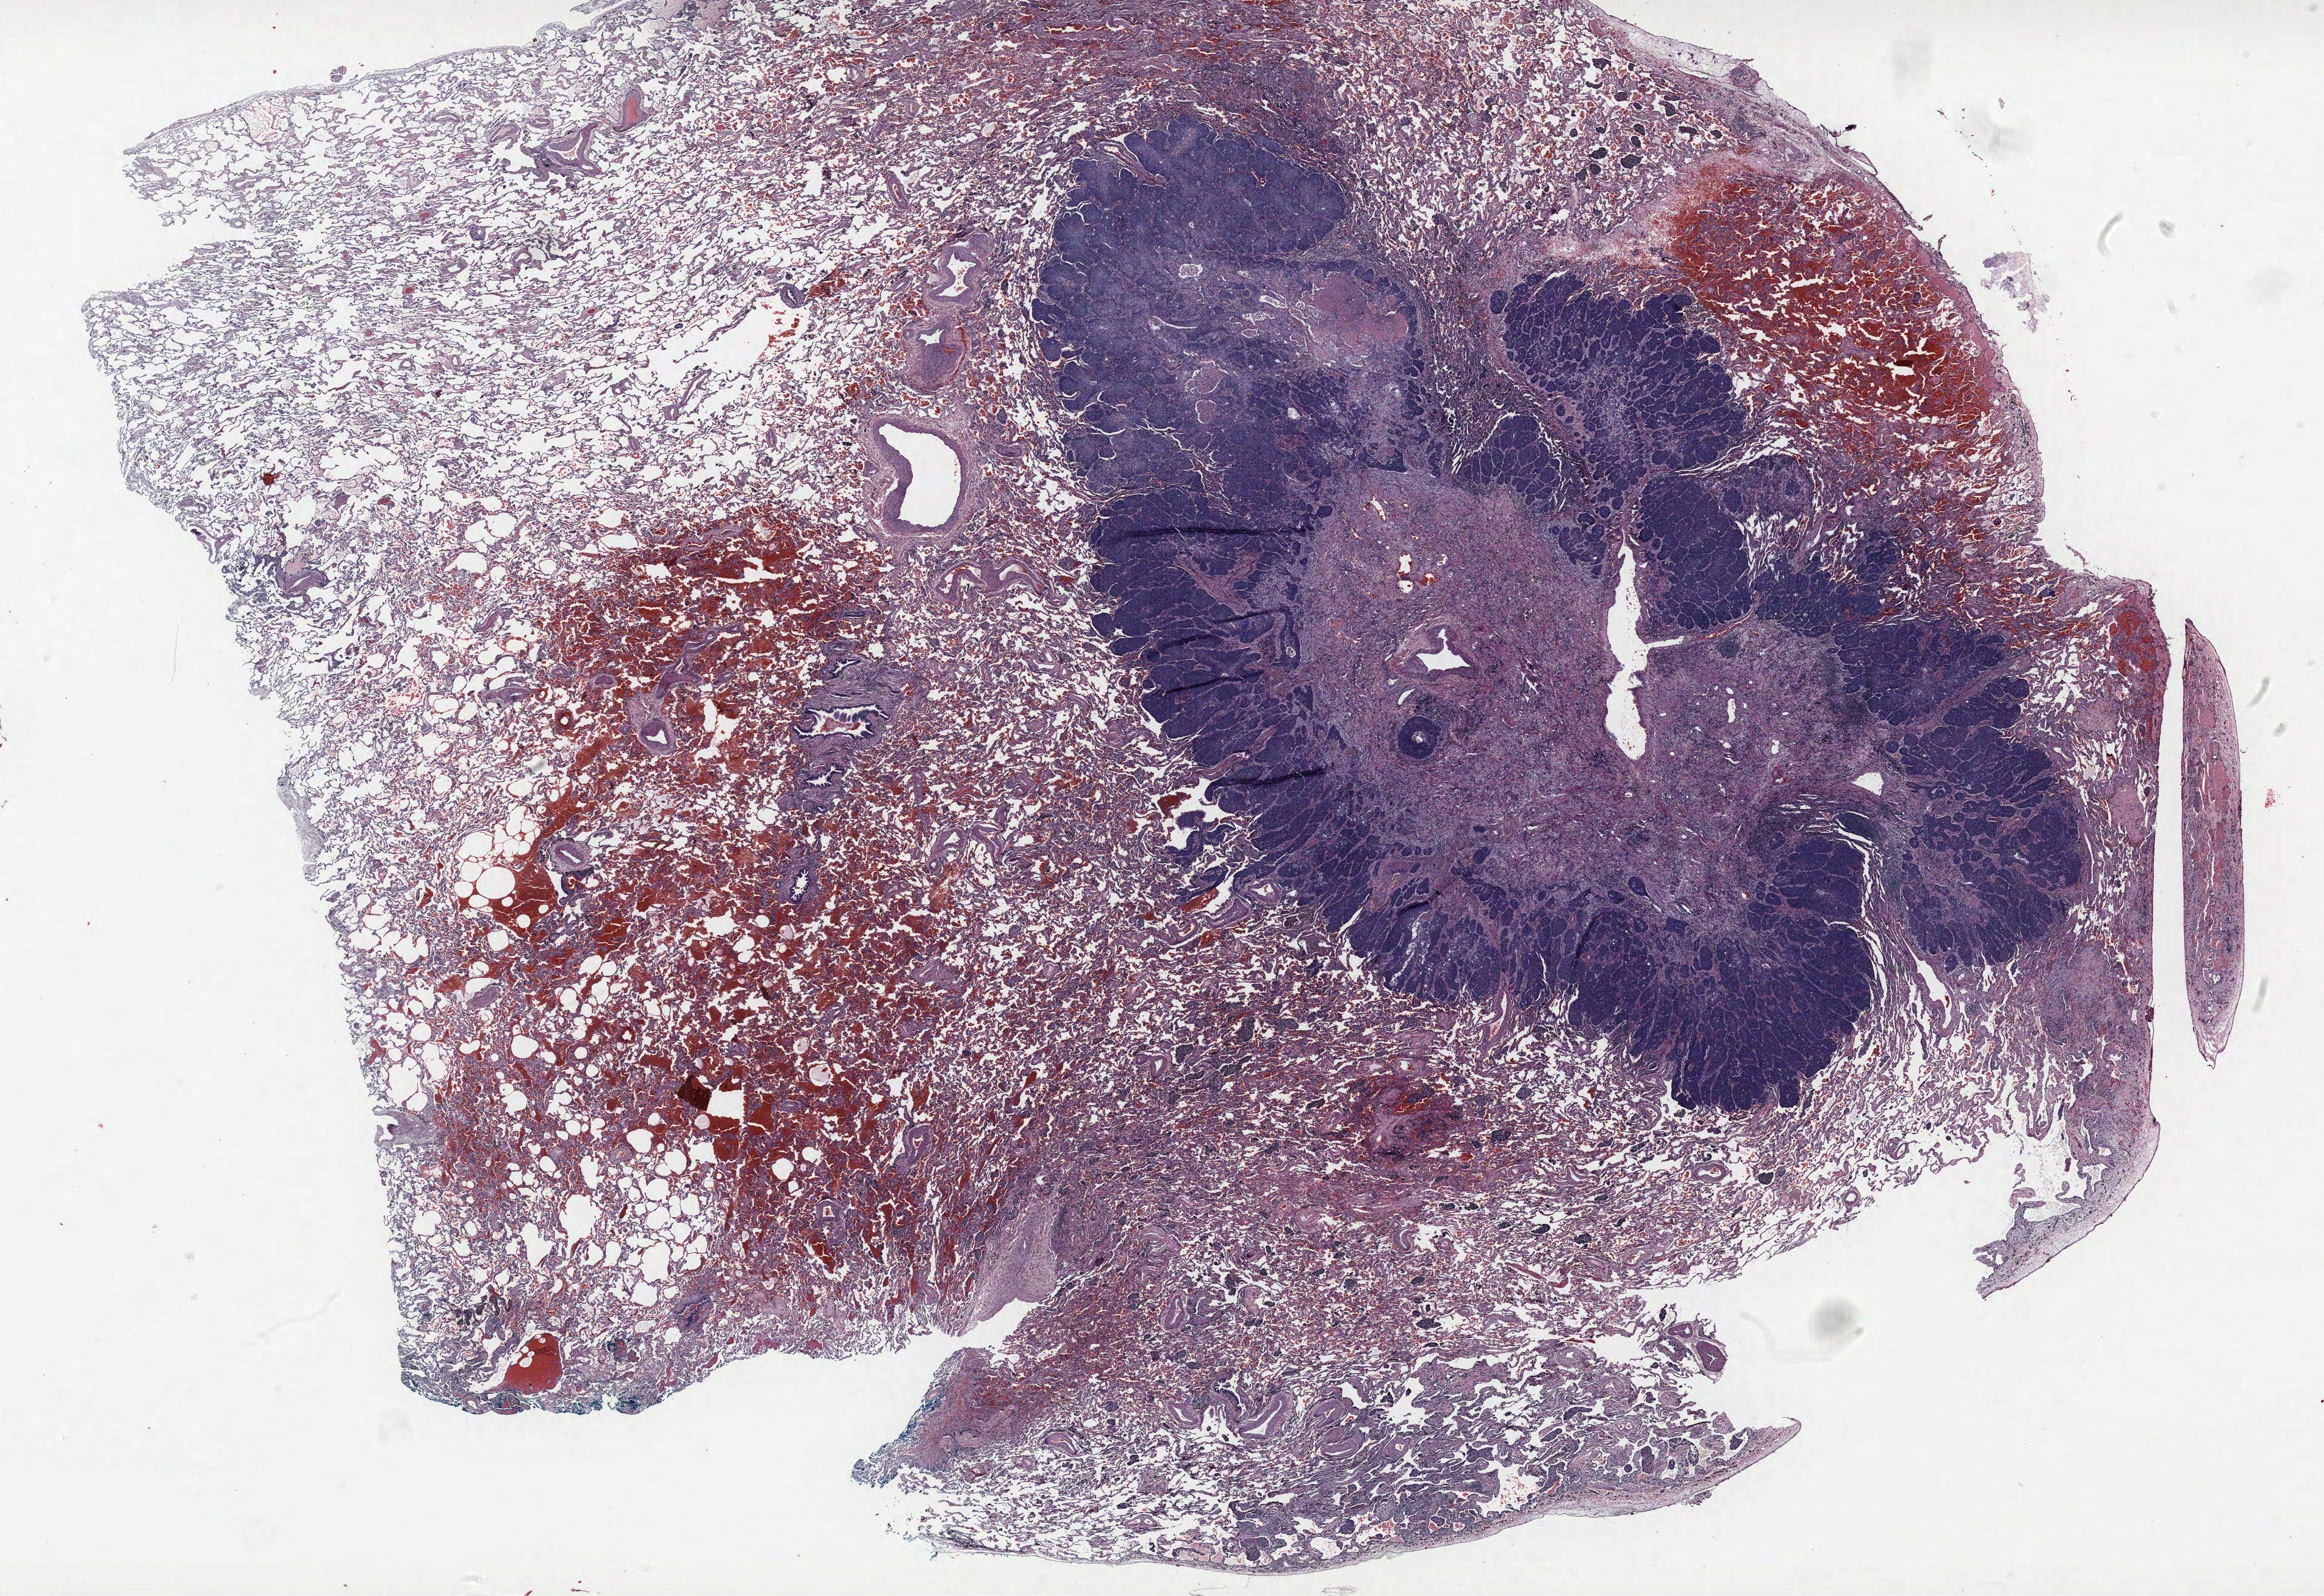
H&E-stained whole-slide image — whole scanned area (about 30.5 x 20.9 mm) shown as a low-resolution overview; formalin-fixed paraffin-embedded (FFPE) section; lung tissue. Male, age 63 at enrolment. Former smoker at enrolment.
Participant's lung-cancer diagnosis: Squamous cell carcinoma, NOS.